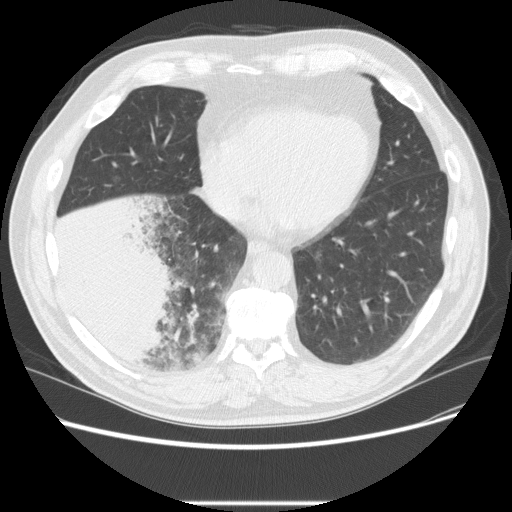
Low-dose screening chest CT, one axial slice. Position 75 of 233 along the scan axis. Reconstruction kernel STANDARD. Lung window (W 1500 / L -600 HU). 2.5 mm slice thickness. 512 × 512 image matrix, field of view 380 × 380 mm.
Annotated regions visible in this slice (expert manual segmentation):
- lesion 3 (tumor, lower lobe of right lung): bounding box <53,196,179,367> (left, top, right, bottom; pixels)